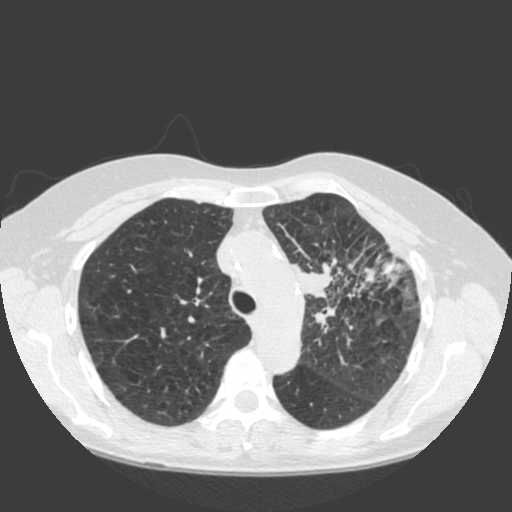
Low-dose screening chest CT, axial slice; baseline annual screen; lung window (W 1500 / L -600 HU); 2 mm slice thickness; slice 46 of 184 in the series. Female participant, aged 66 years at enrolment. Current smoker at enrolment.
- Lesion marked by an expert reader, bounding box [x1, y1, x2, y2] px = [286, 243, 397, 341].
- The exam's reader record, not a measurement of the box and not confirmed to be the same lesion: non-calcified nodule or mass ≥4 mm, left upper lobe, 61 × 45 mm, spiculated (stellate) margins, soft tissue attenuation.
- Later outcome: lung cancer diagnosed 19 days after this screen — squamous cell carcinoma, keratinizing, NOS, left upper lobe, left hilum, mediastinum, left main stem bronchus, other location, poorly differentiated (G3), stage IIIB (AJCC 6th edition), 60 mm at pathology.